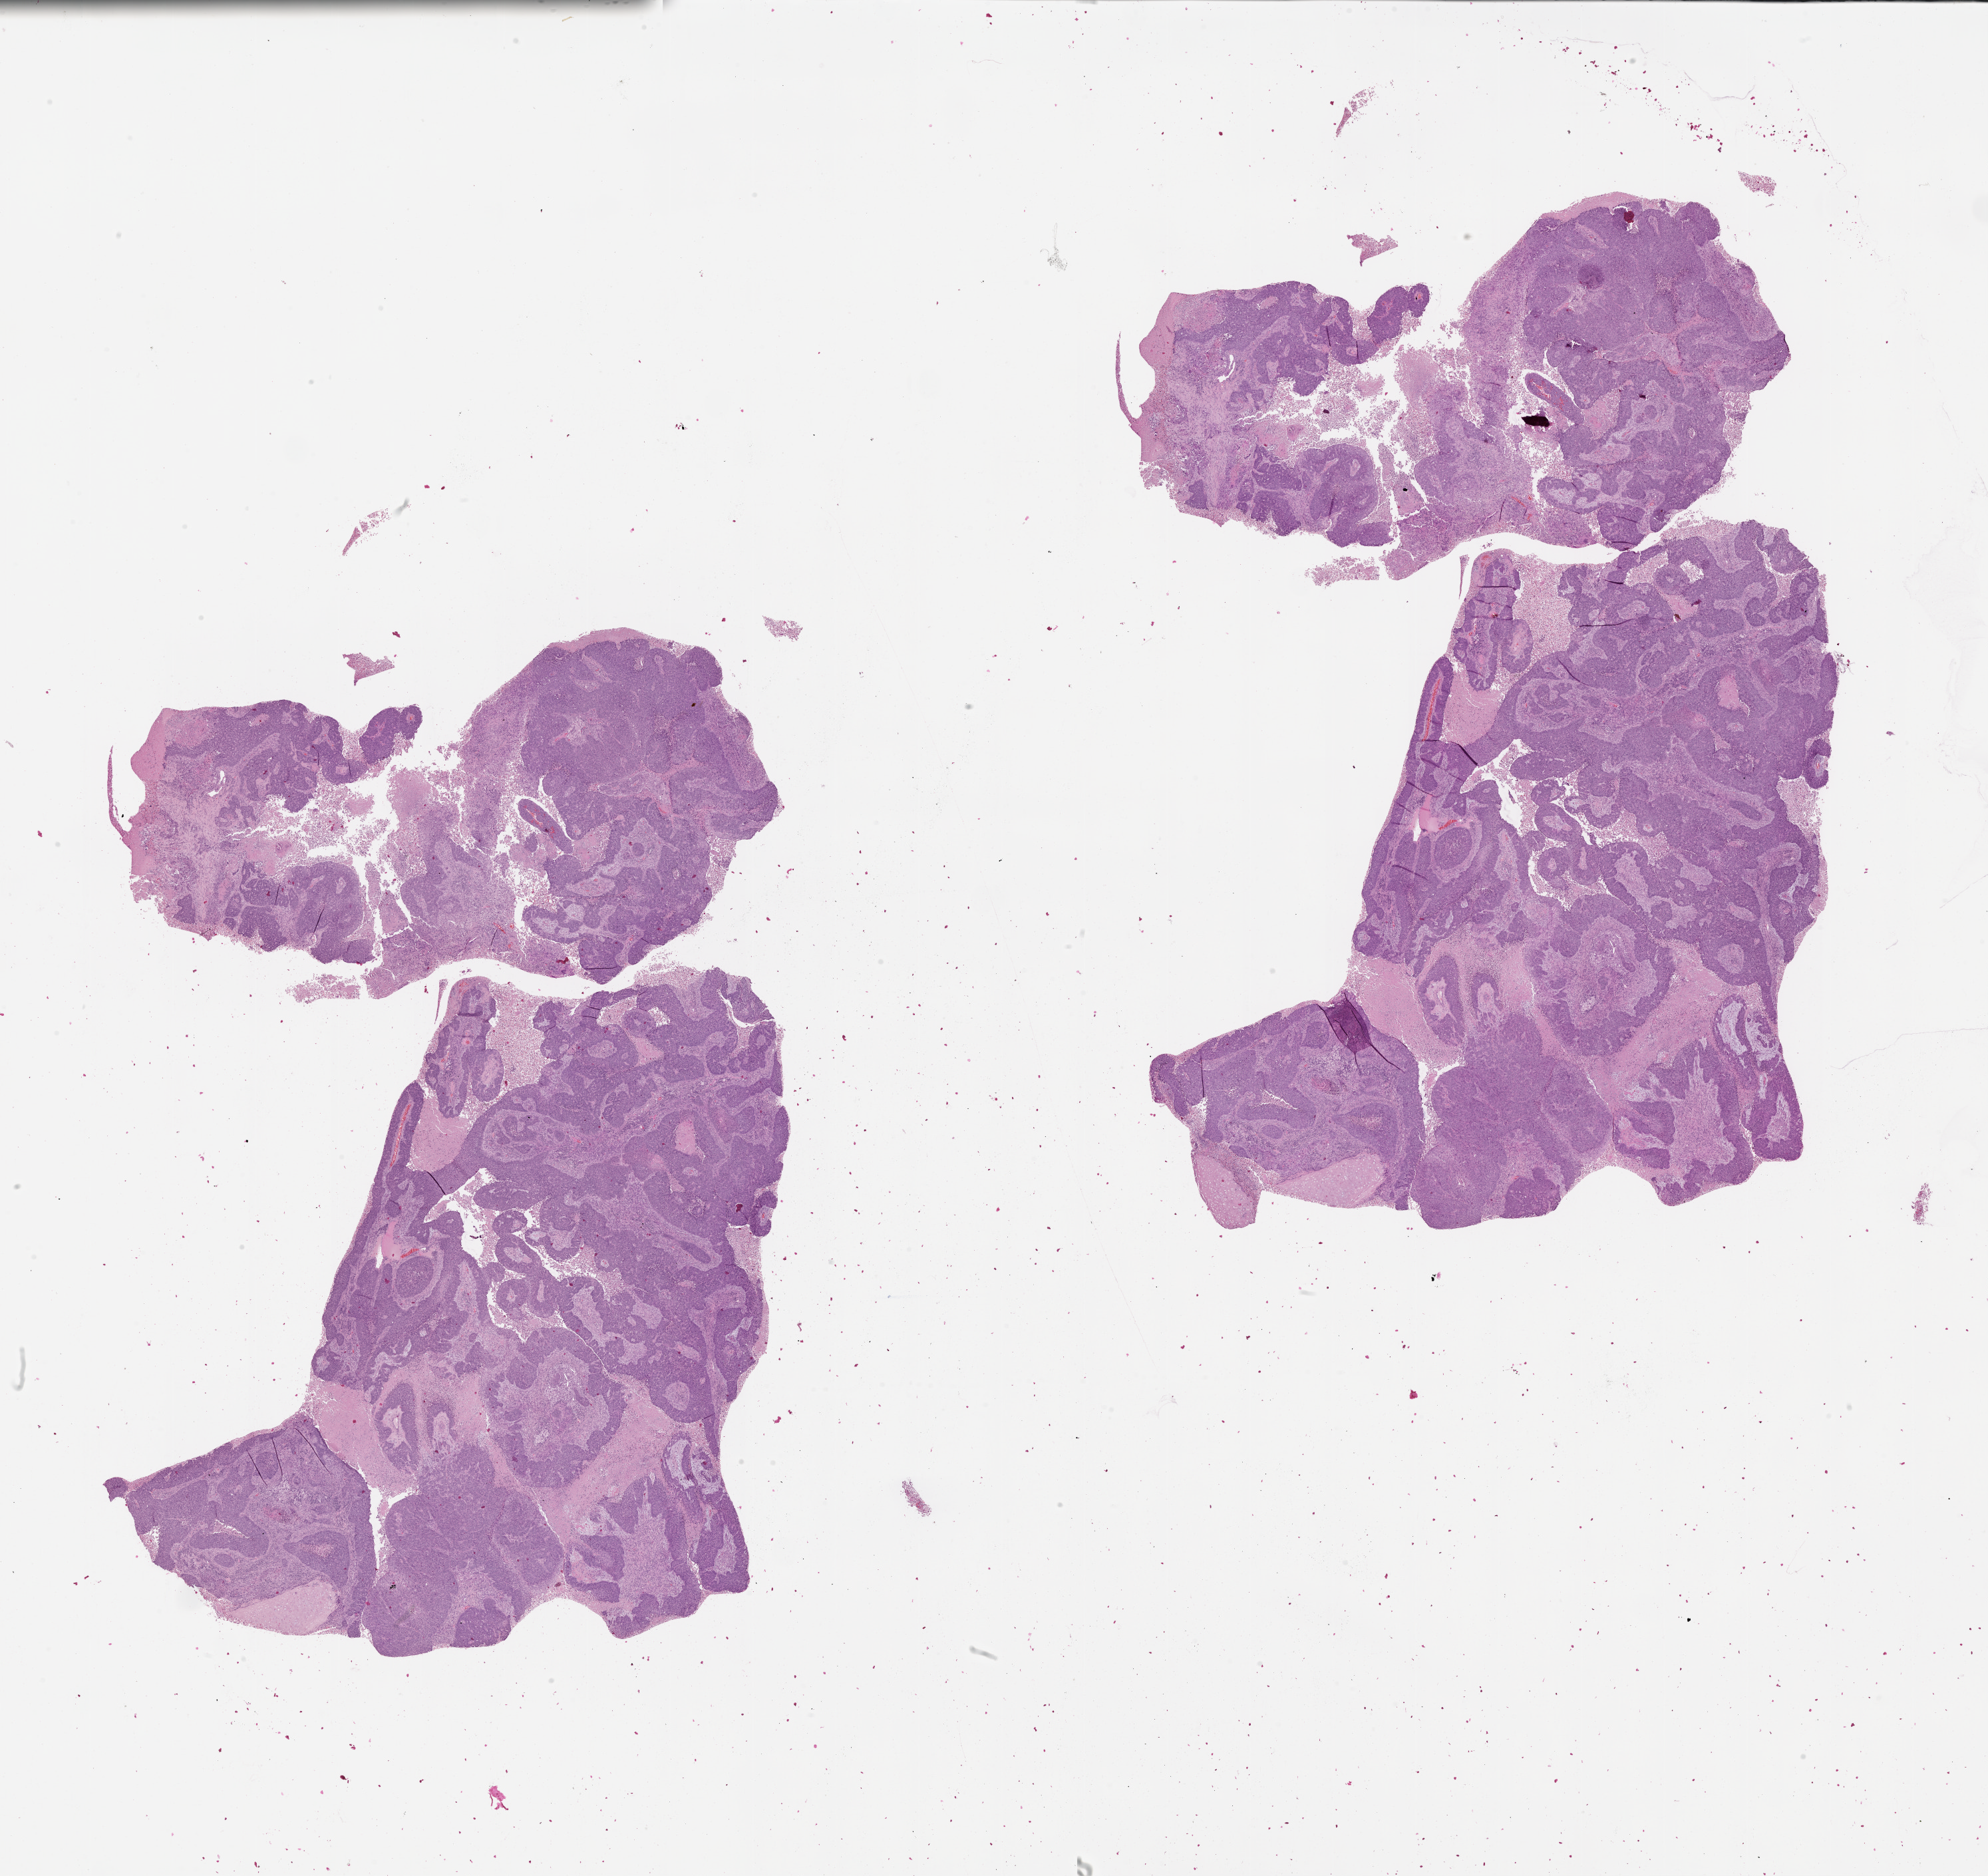
Whole-slide histology image, Hematoxylin and eosin (H&E) stained — low-resolution overview of the scanned area, about 24.1 x 22.7 mm. Tumour tissue sample, lung. Male, 69 y/o.
Patient diagnosis (cohort enrolment): squamous cell carcinoma (lung).